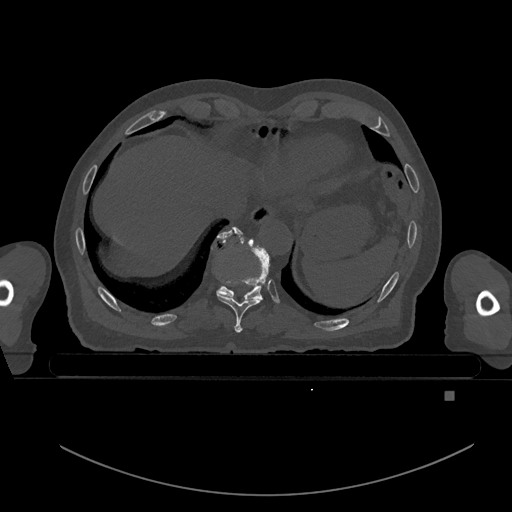
CT including the spine, one axial slice; position 122 of 969 along the scan axis; bone window (W 1800 / L 400 HU); 512 × 512 image matrix. Male patient, age 82 years. From the clinical record (not read from this slice): primary cancer: prostate; vertebrae with lytic lesions (as recorded): T11, T9, T8, T2.
Structures marked on this image (semi-automatically segmented with operator editing):
- T10 vertebra: box from (x=218, y=226) to (x=270, y=299) px
- T9 vertebra: (x=216, y=230)–(x=263, y=333)